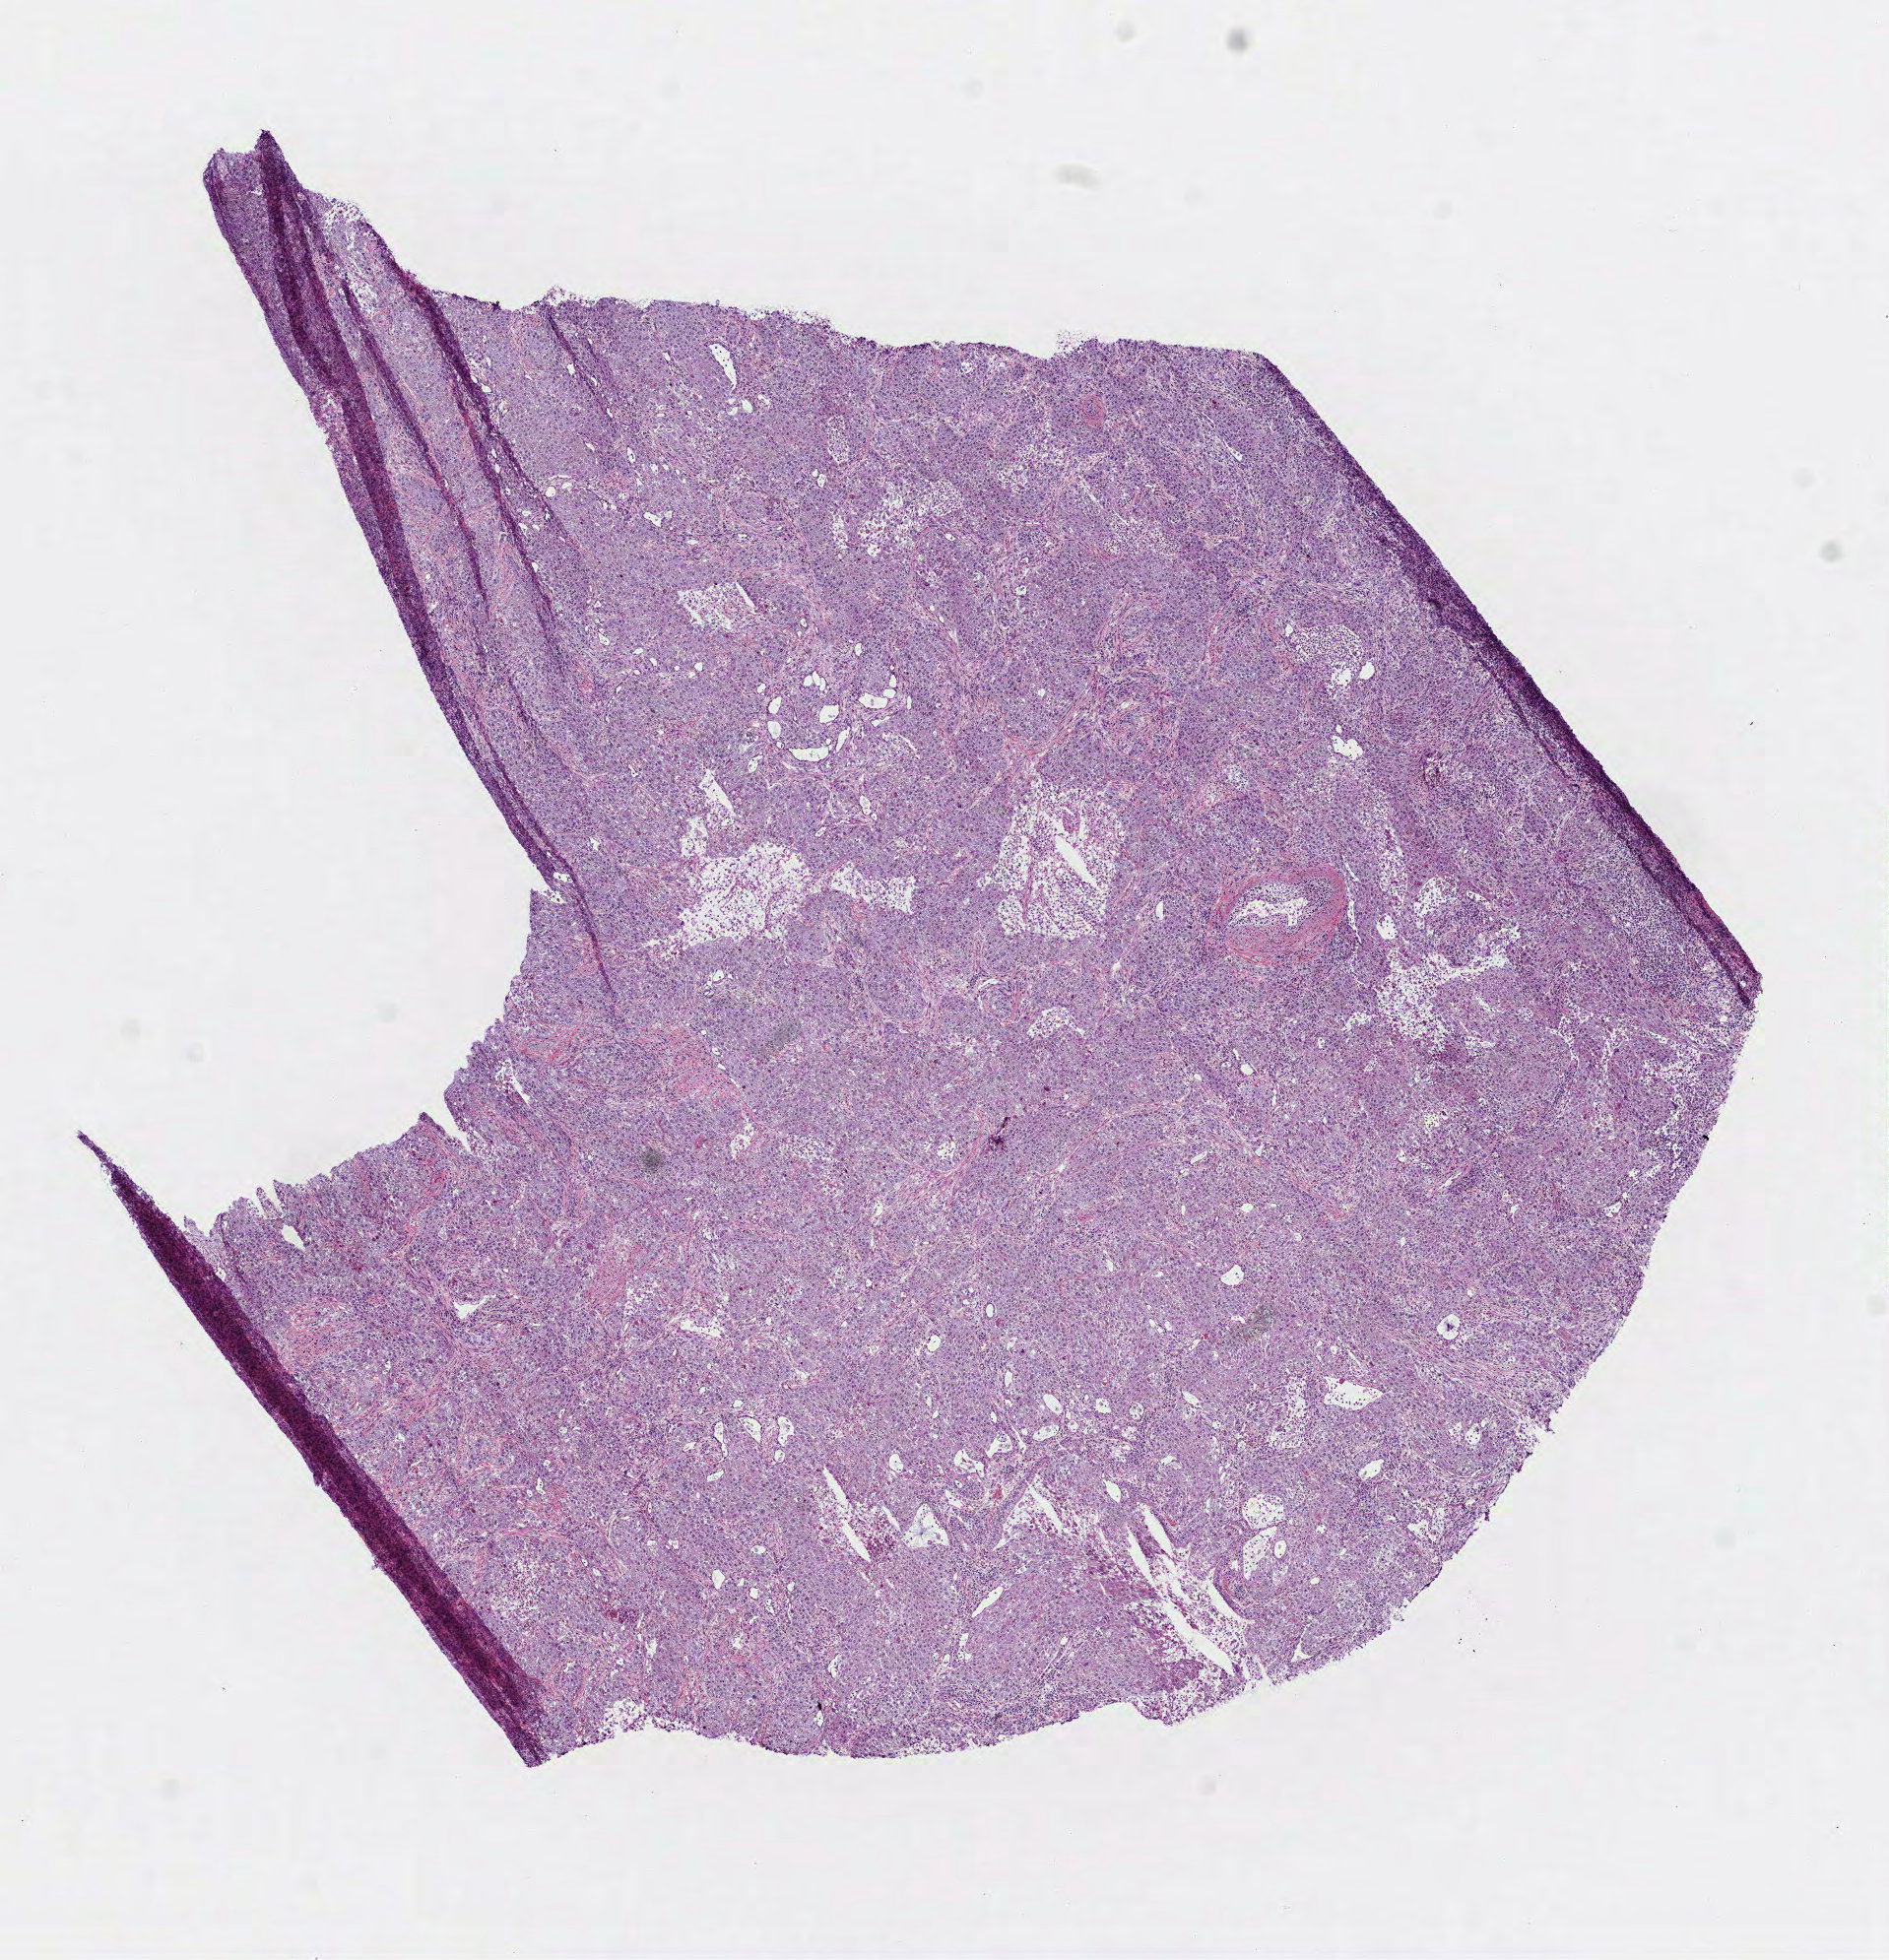
Hematoxylin and eosin (H&E) stained whole-slide image — a low-resolution overview of the entire scanned area, about 7.7 x 8.0 mm (acquisition: 40x scan), frozen section, lung, primary tumour sample. Patient: male, age at initial diagnosis 71 years. Composition of this section per pathologist review: tumour cells 82%, tumour nuclei 75%.
Diagnosis: Squamous cell carcinoma, NOS (lower lobe, lung).